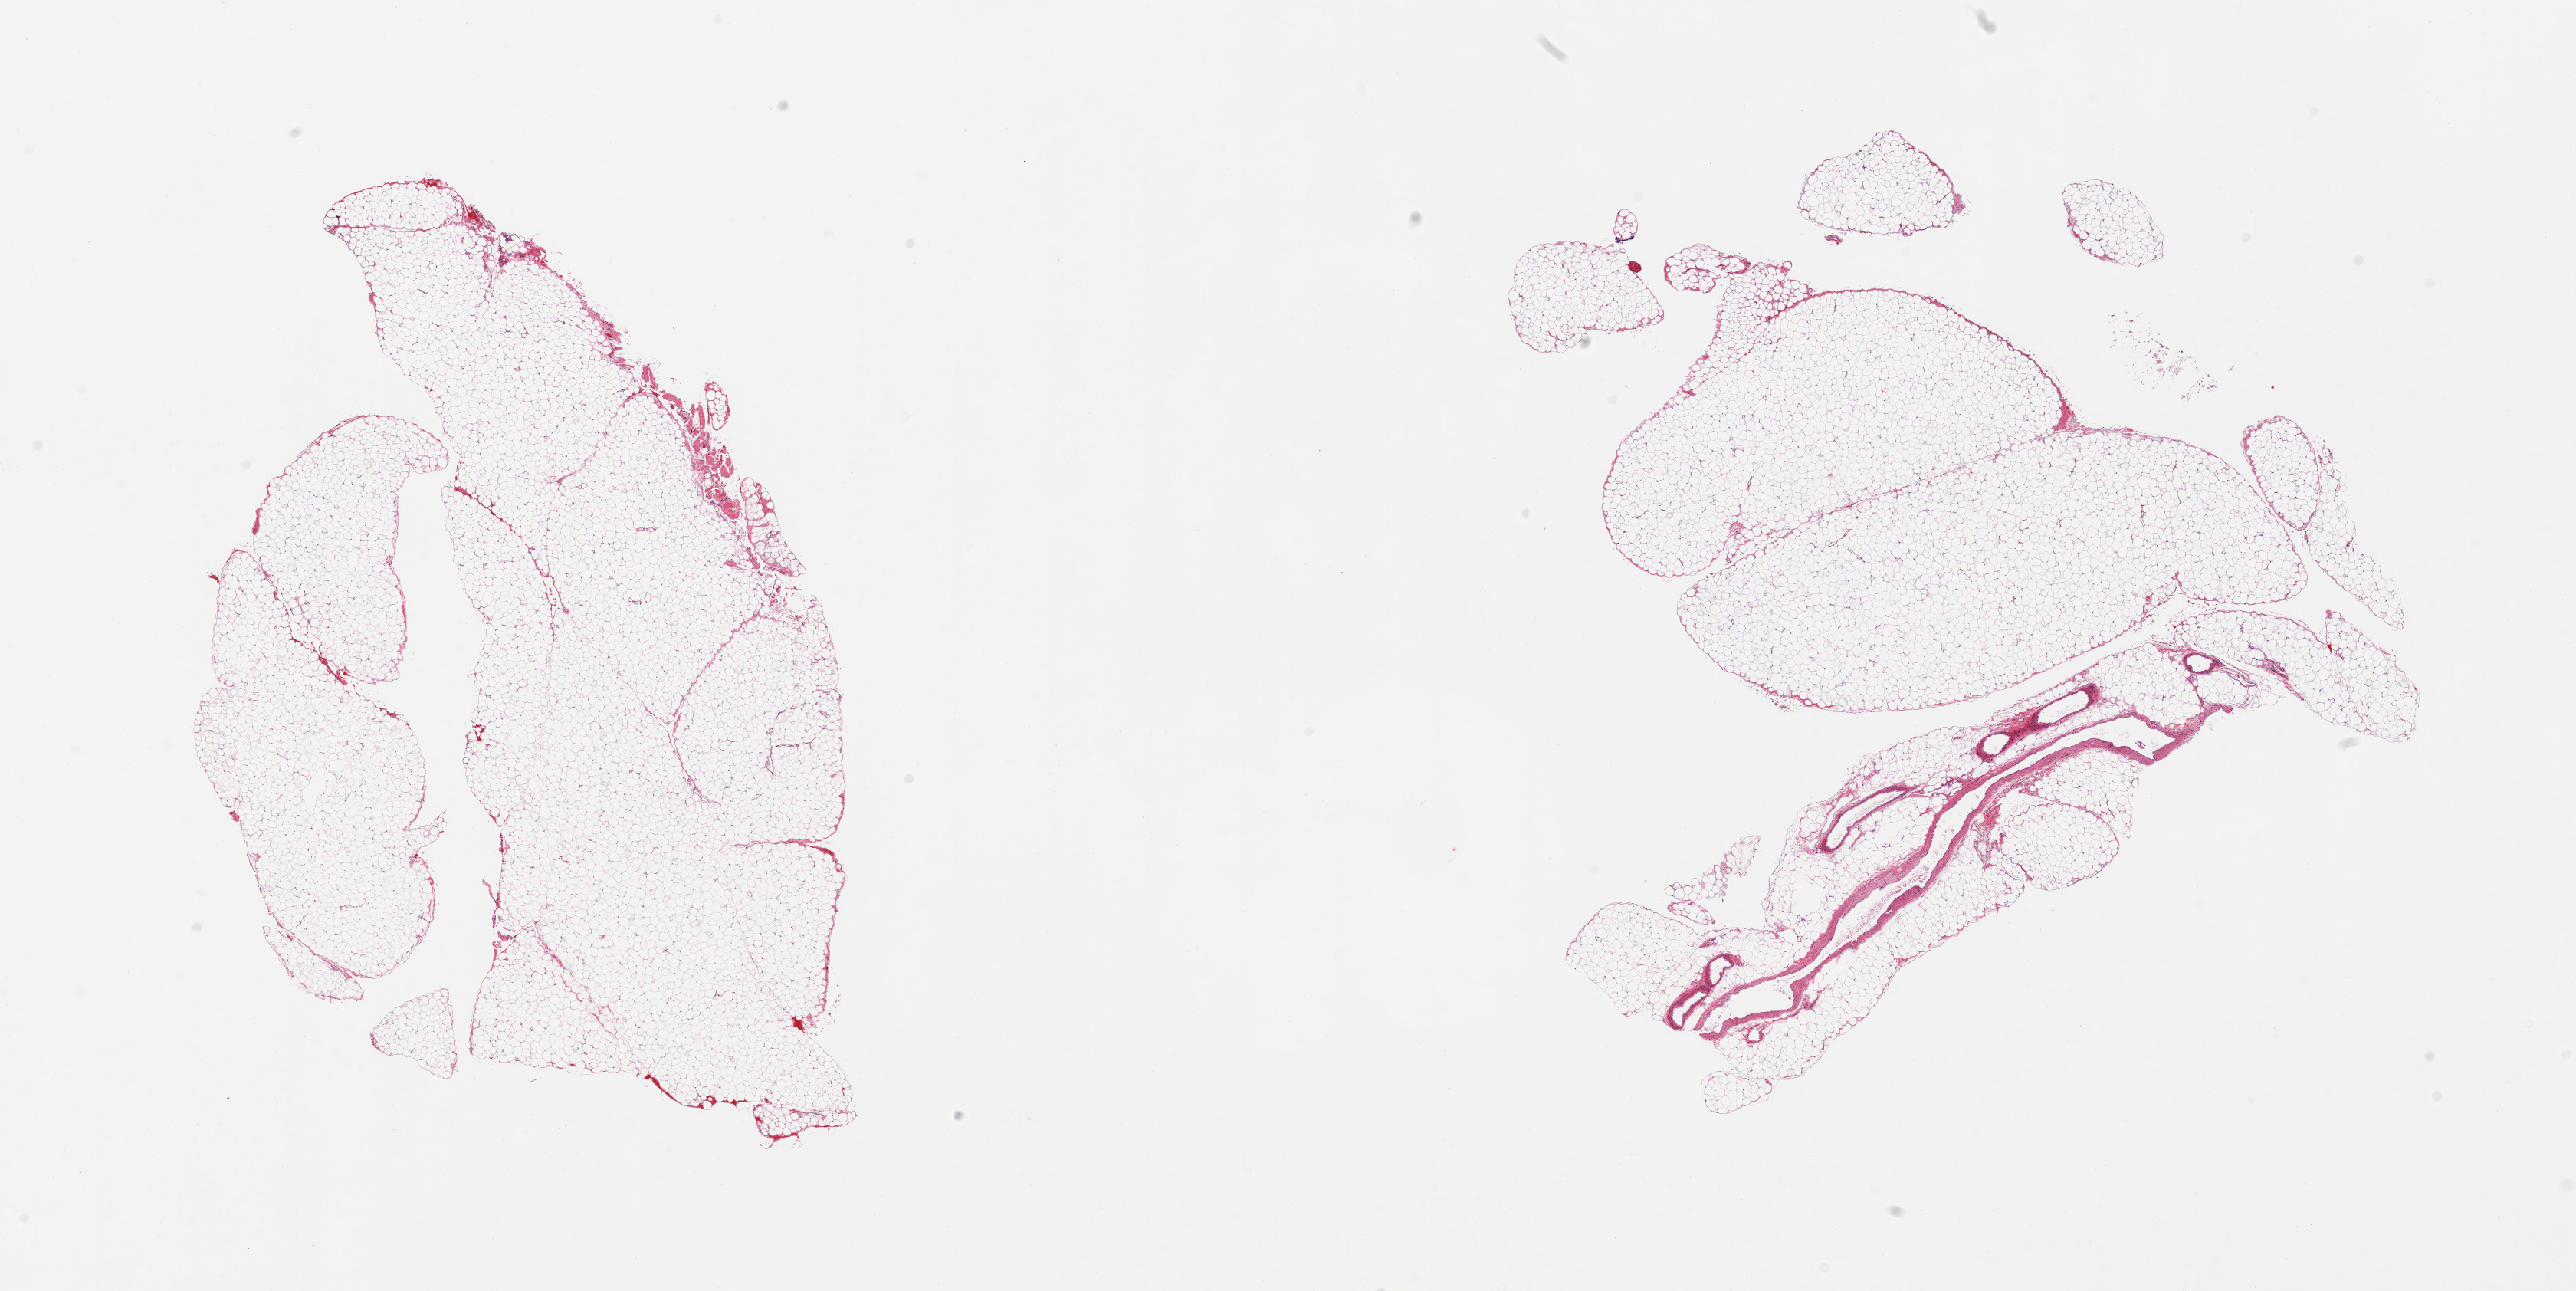
Haematoxylin and eosin whole-slide image, brightfield, a low-resolution overview of the entire scanned area, about 26.6 x 13.3 mm, PAXgene-fixed, paraffin-embedded tissue, sampled site (target tissue): omentum, donor tissue sample. Donor: male.
• reviewer comment on this tissue sample: 2 pieces